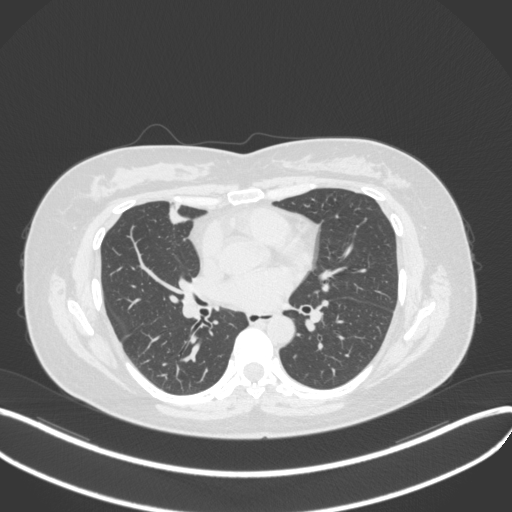
Chest CT, one axial slice; position 159 of 272 along the scan axis; 120 kVp; lung window (W 1500 / L -600 HU); 1 mm slice thickness; 512 × 512 image matrix, field of view 400 × 400 mm. Patient: female, 42 years. From the clinical record (not read from this slice): clinical TNM (as recorded): T1b N0 M0.
Outlined on this slice (rectangle marked by the reading radiologist):
- lung tumour (recorded histology: adenocarcinoma): bounding box <165,202,196,228> (left, top, right, bottom; pixels)